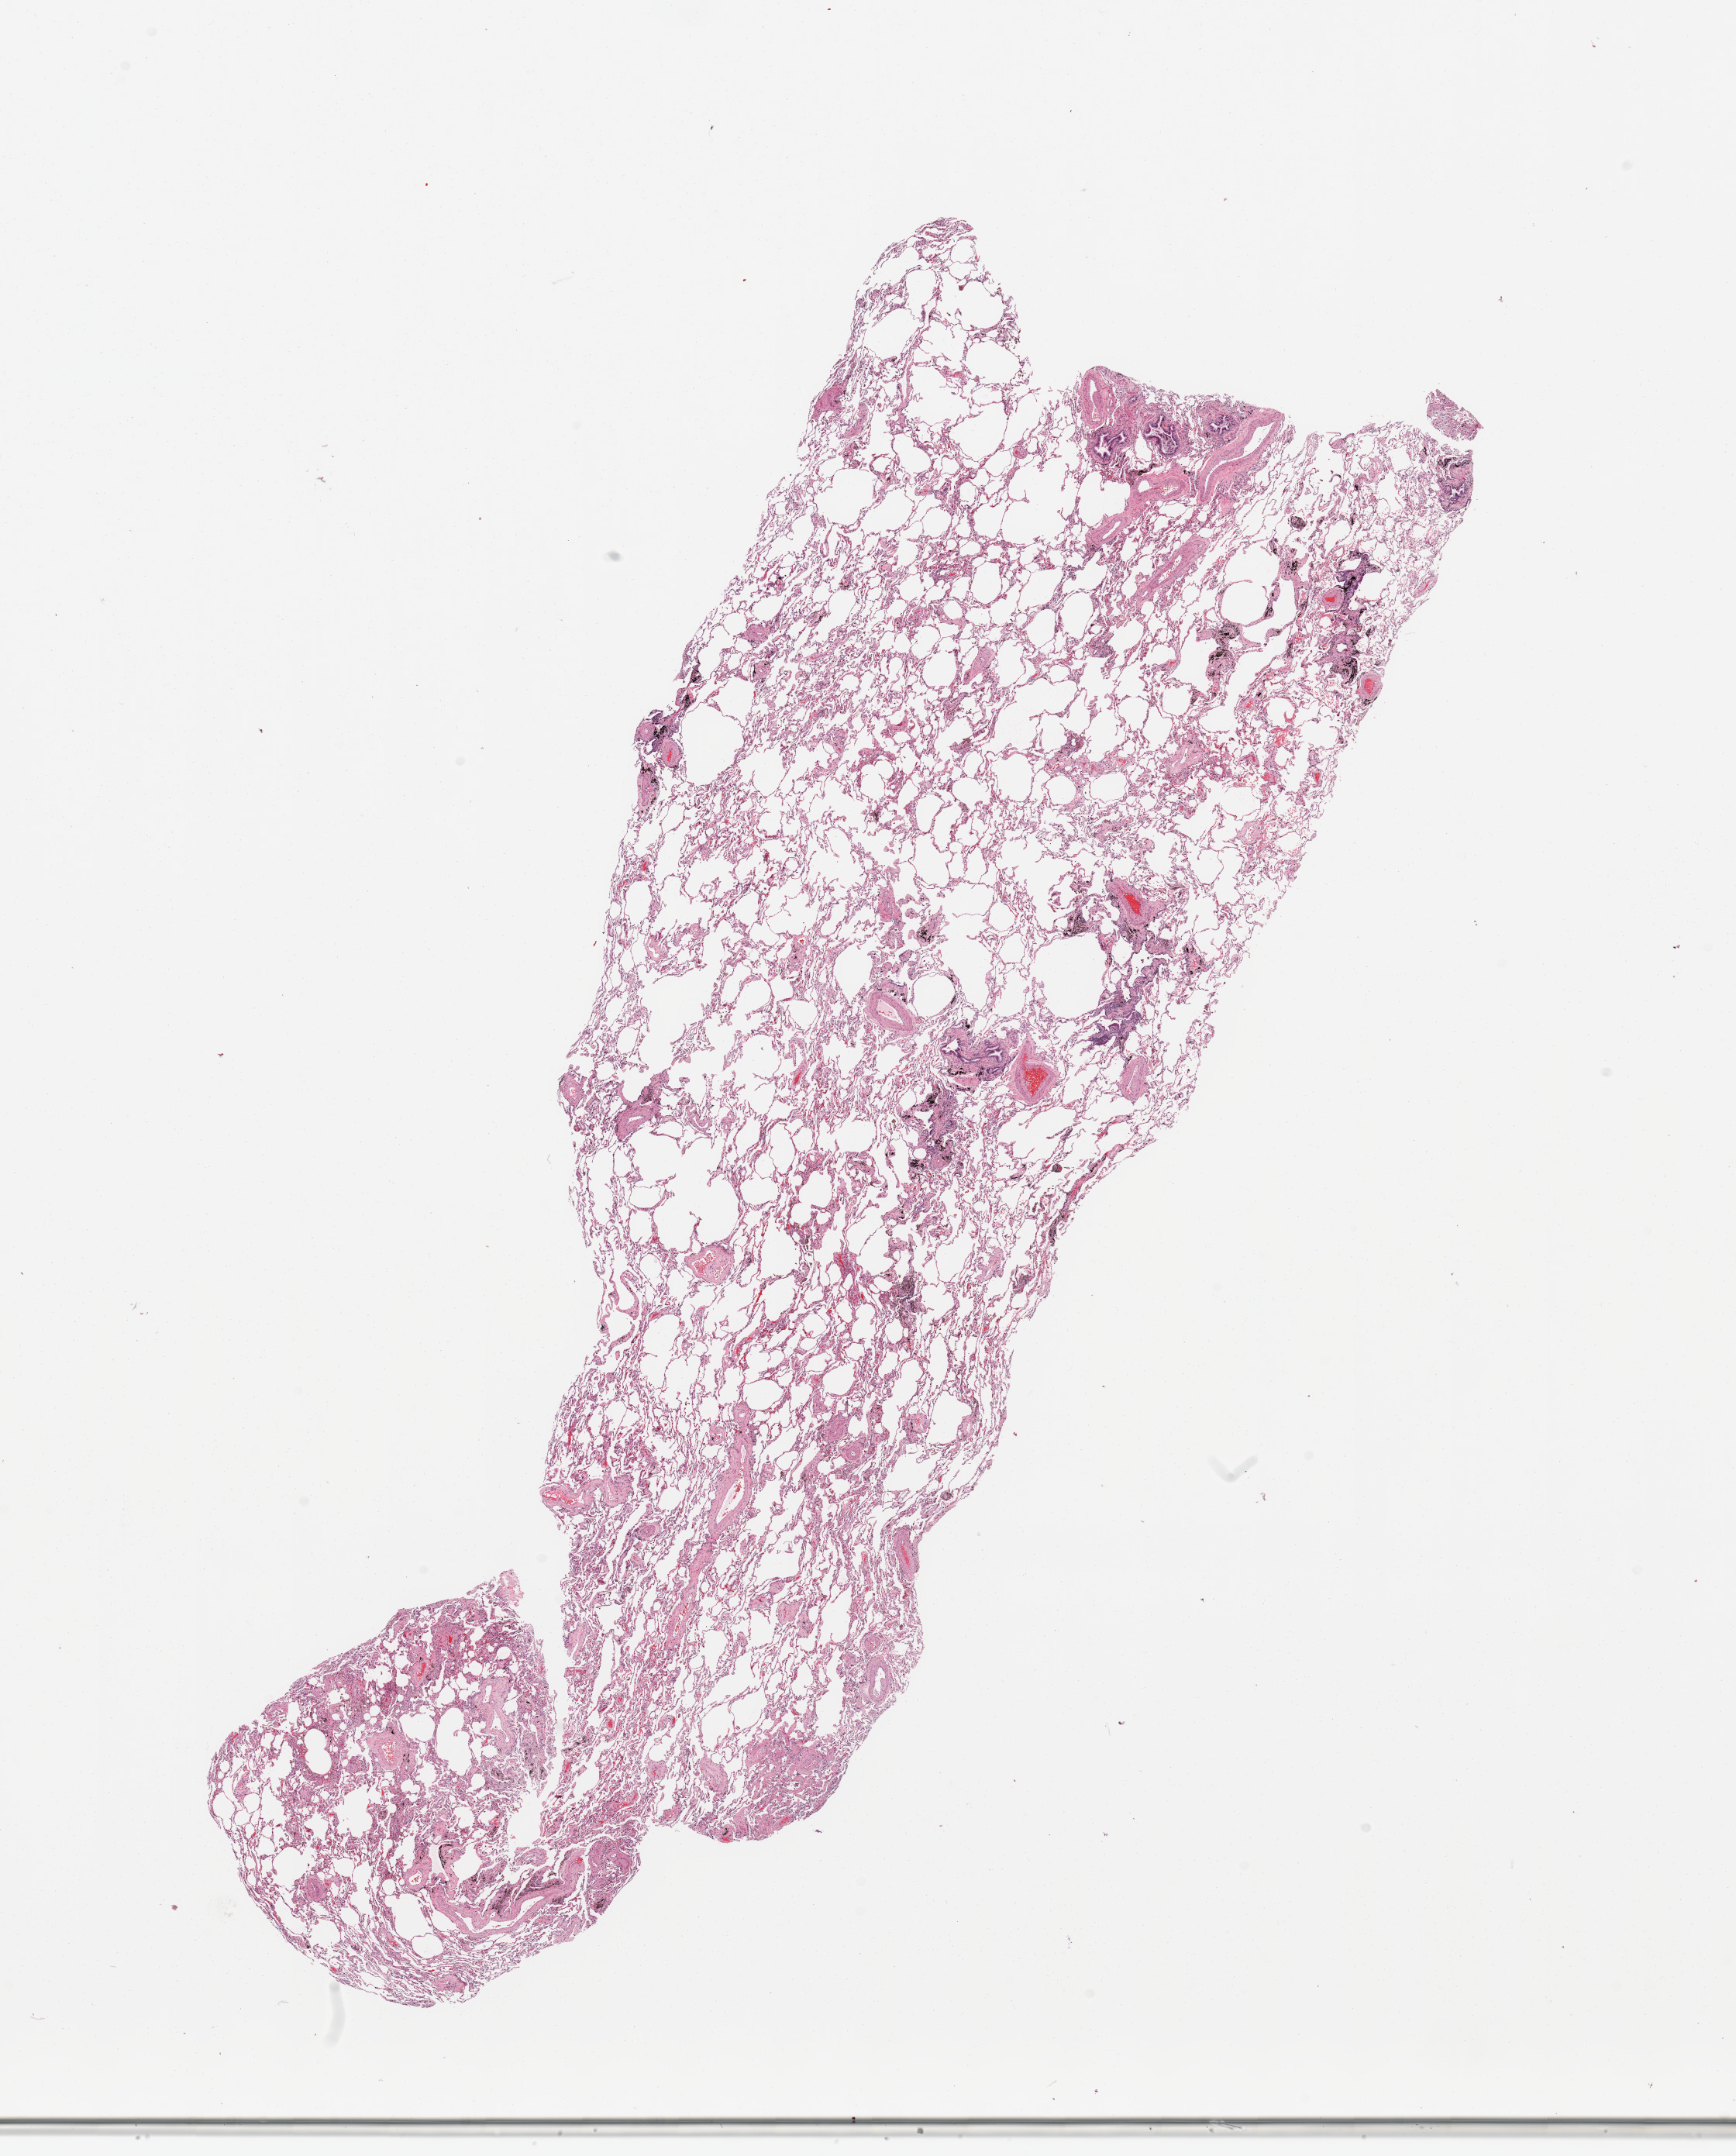
Digitized H&E-stained tissue section (whole slide) — whole scanned area (about 17.7 x 22.0 mm) shown as a low-resolution overview. Normal (non-tumour) tissue sample, sampled site: lung. Patient: female, age 58 years.
This section: normal (non-tumour) tissue from the same patient. Patient diagnosis: Adenocarcinoma, NOS.